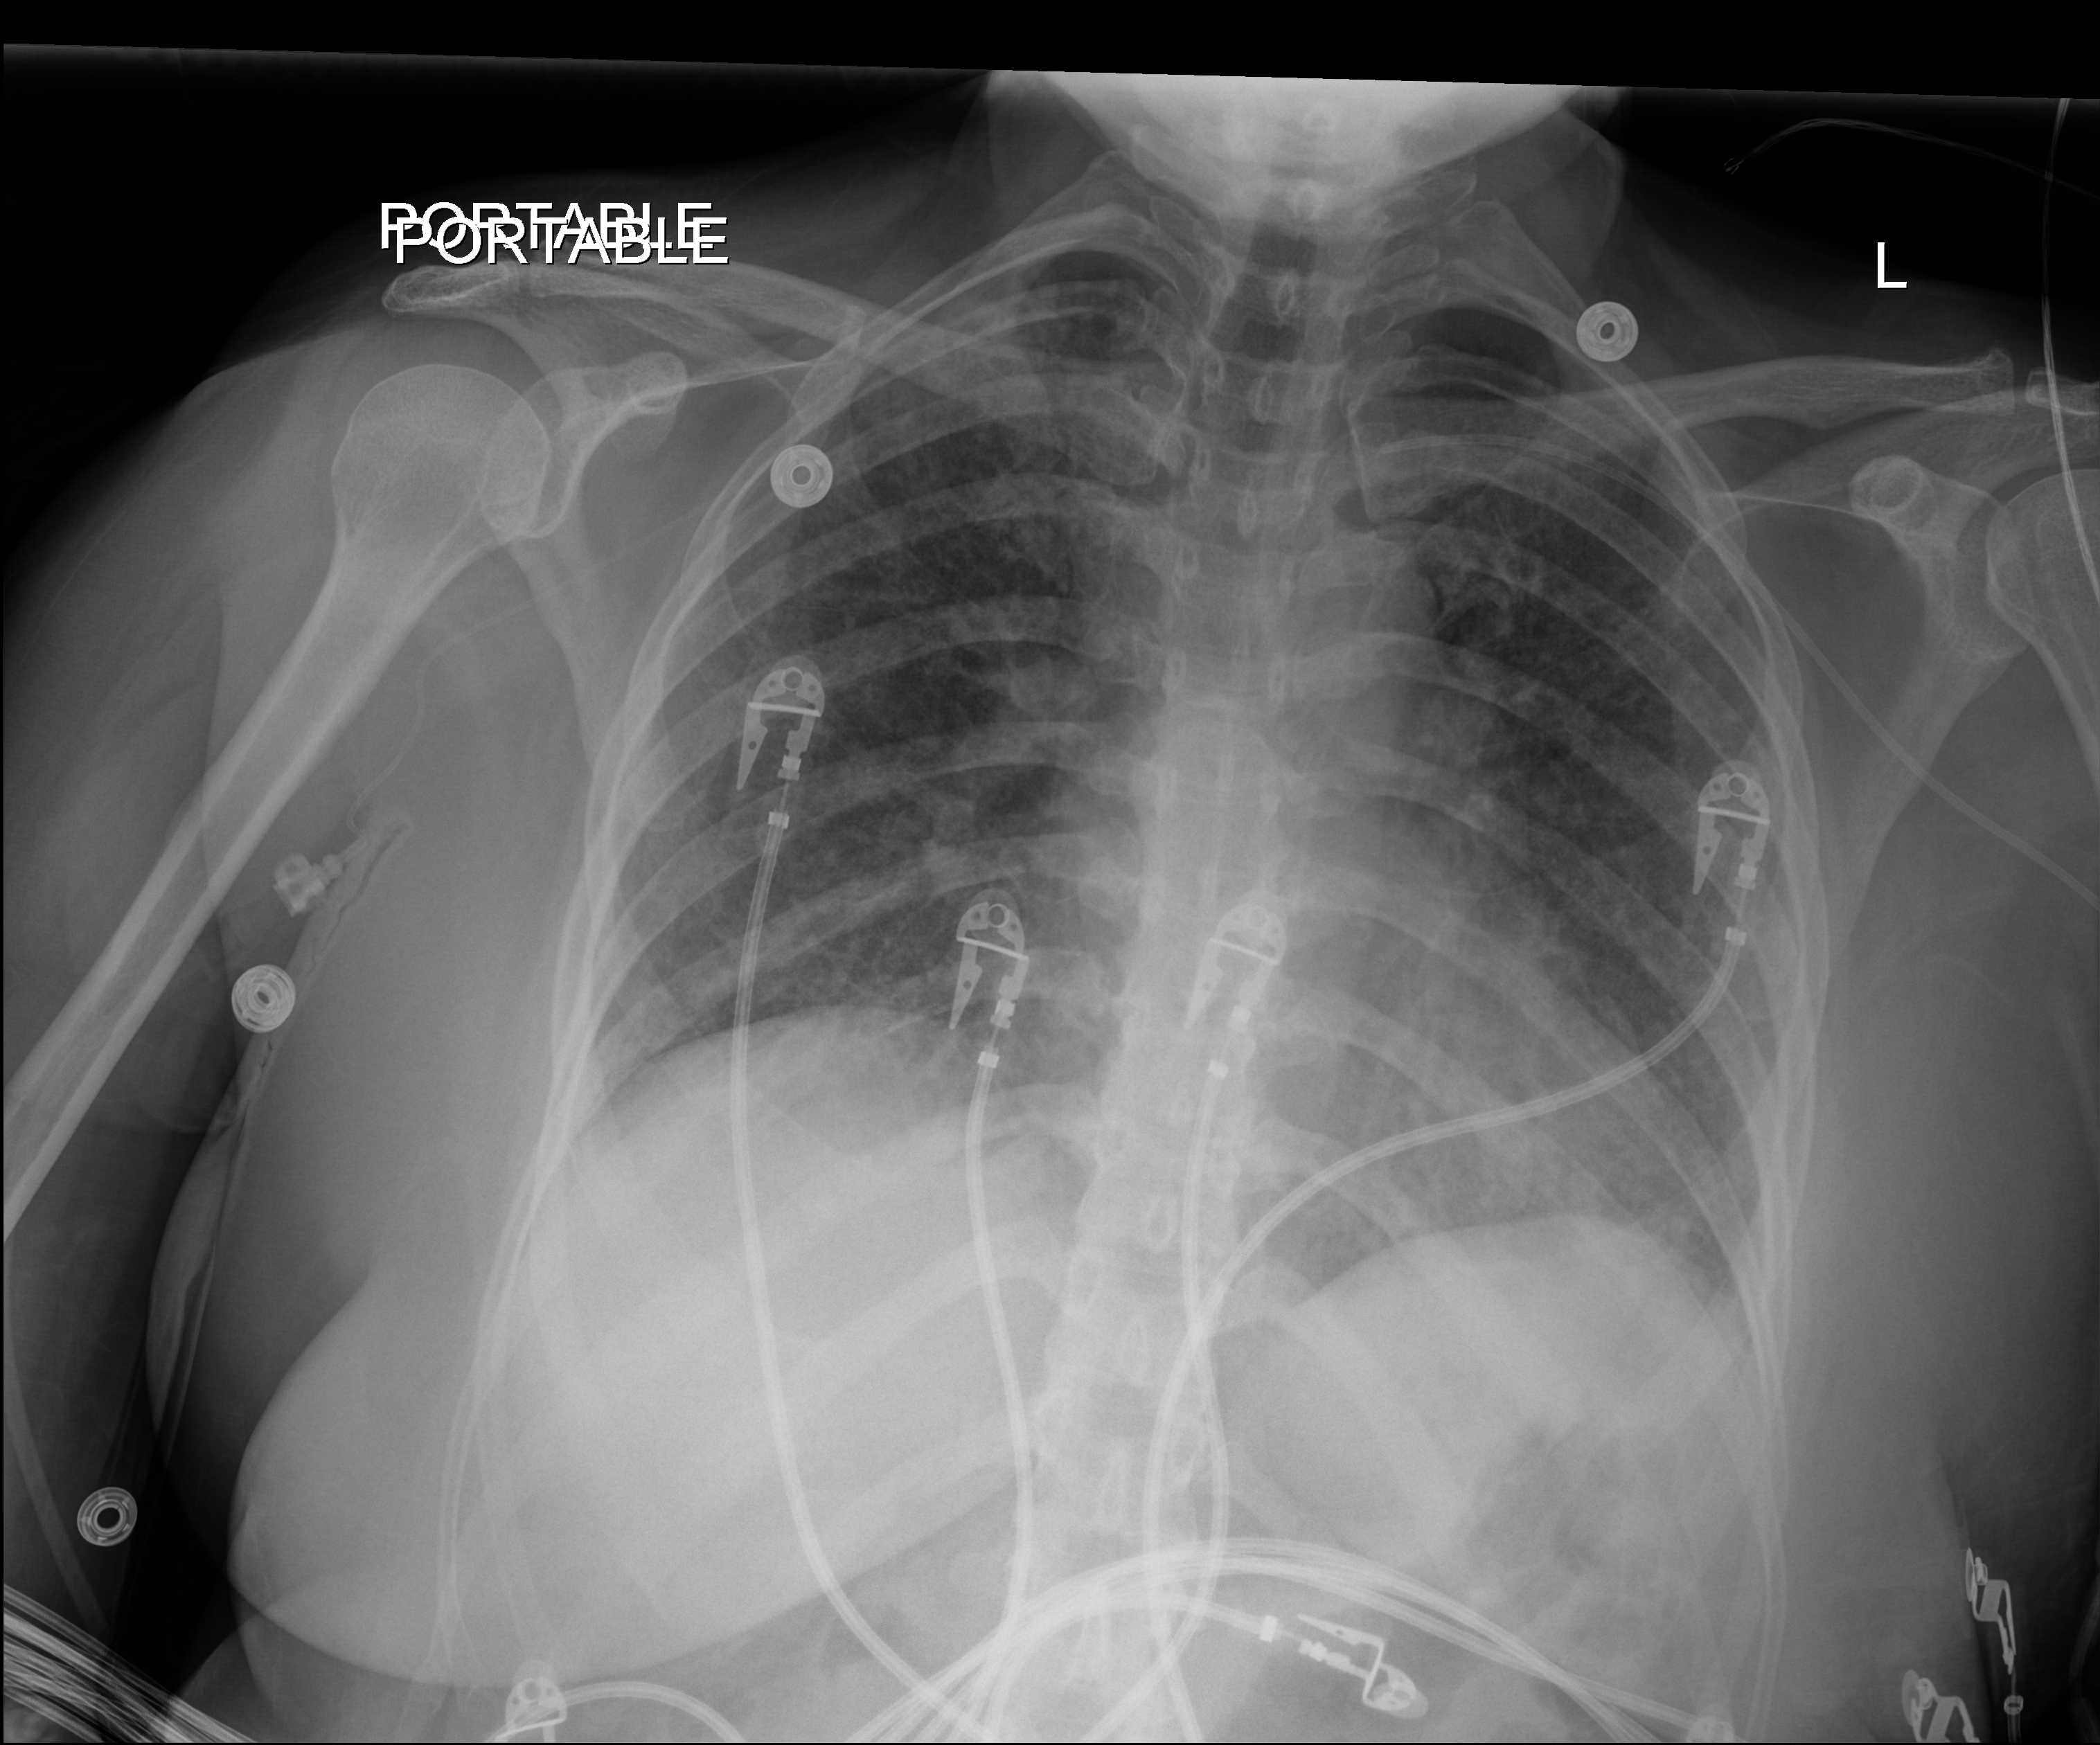
Chest X-ray (portable), anteroposterior (AP) projection. Patient hospitalised with COVID-19; male, aged 18–59 years.
Hospital-stay facts (about this admission, not read from this image; timing relative to this image not recorded):
- hypertension (admission record): yes
- other chronic lung disease (admission record): no
- length of hospital stay: 38 days